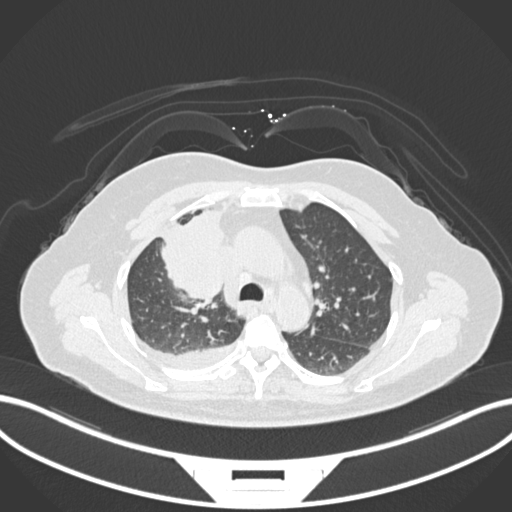
Chest CT, one axial slice; position 107 of 172 along the scan axis; 120 kVp; lung window (W 1500 / L -600 HU); 512 × 512 image matrix. Female patient, age 52 years. Case-level facts recorded for this patient, not image findings: clinical TNM (as recorded): T3 N1 M1.
Structures marked on this image (bounding box drawn by a radiologist):
- lung tumour (recorded histology: adenocarcinoma): bounding box (x1, y1, x2, y2) in pixels: (157, 206, 227, 306)